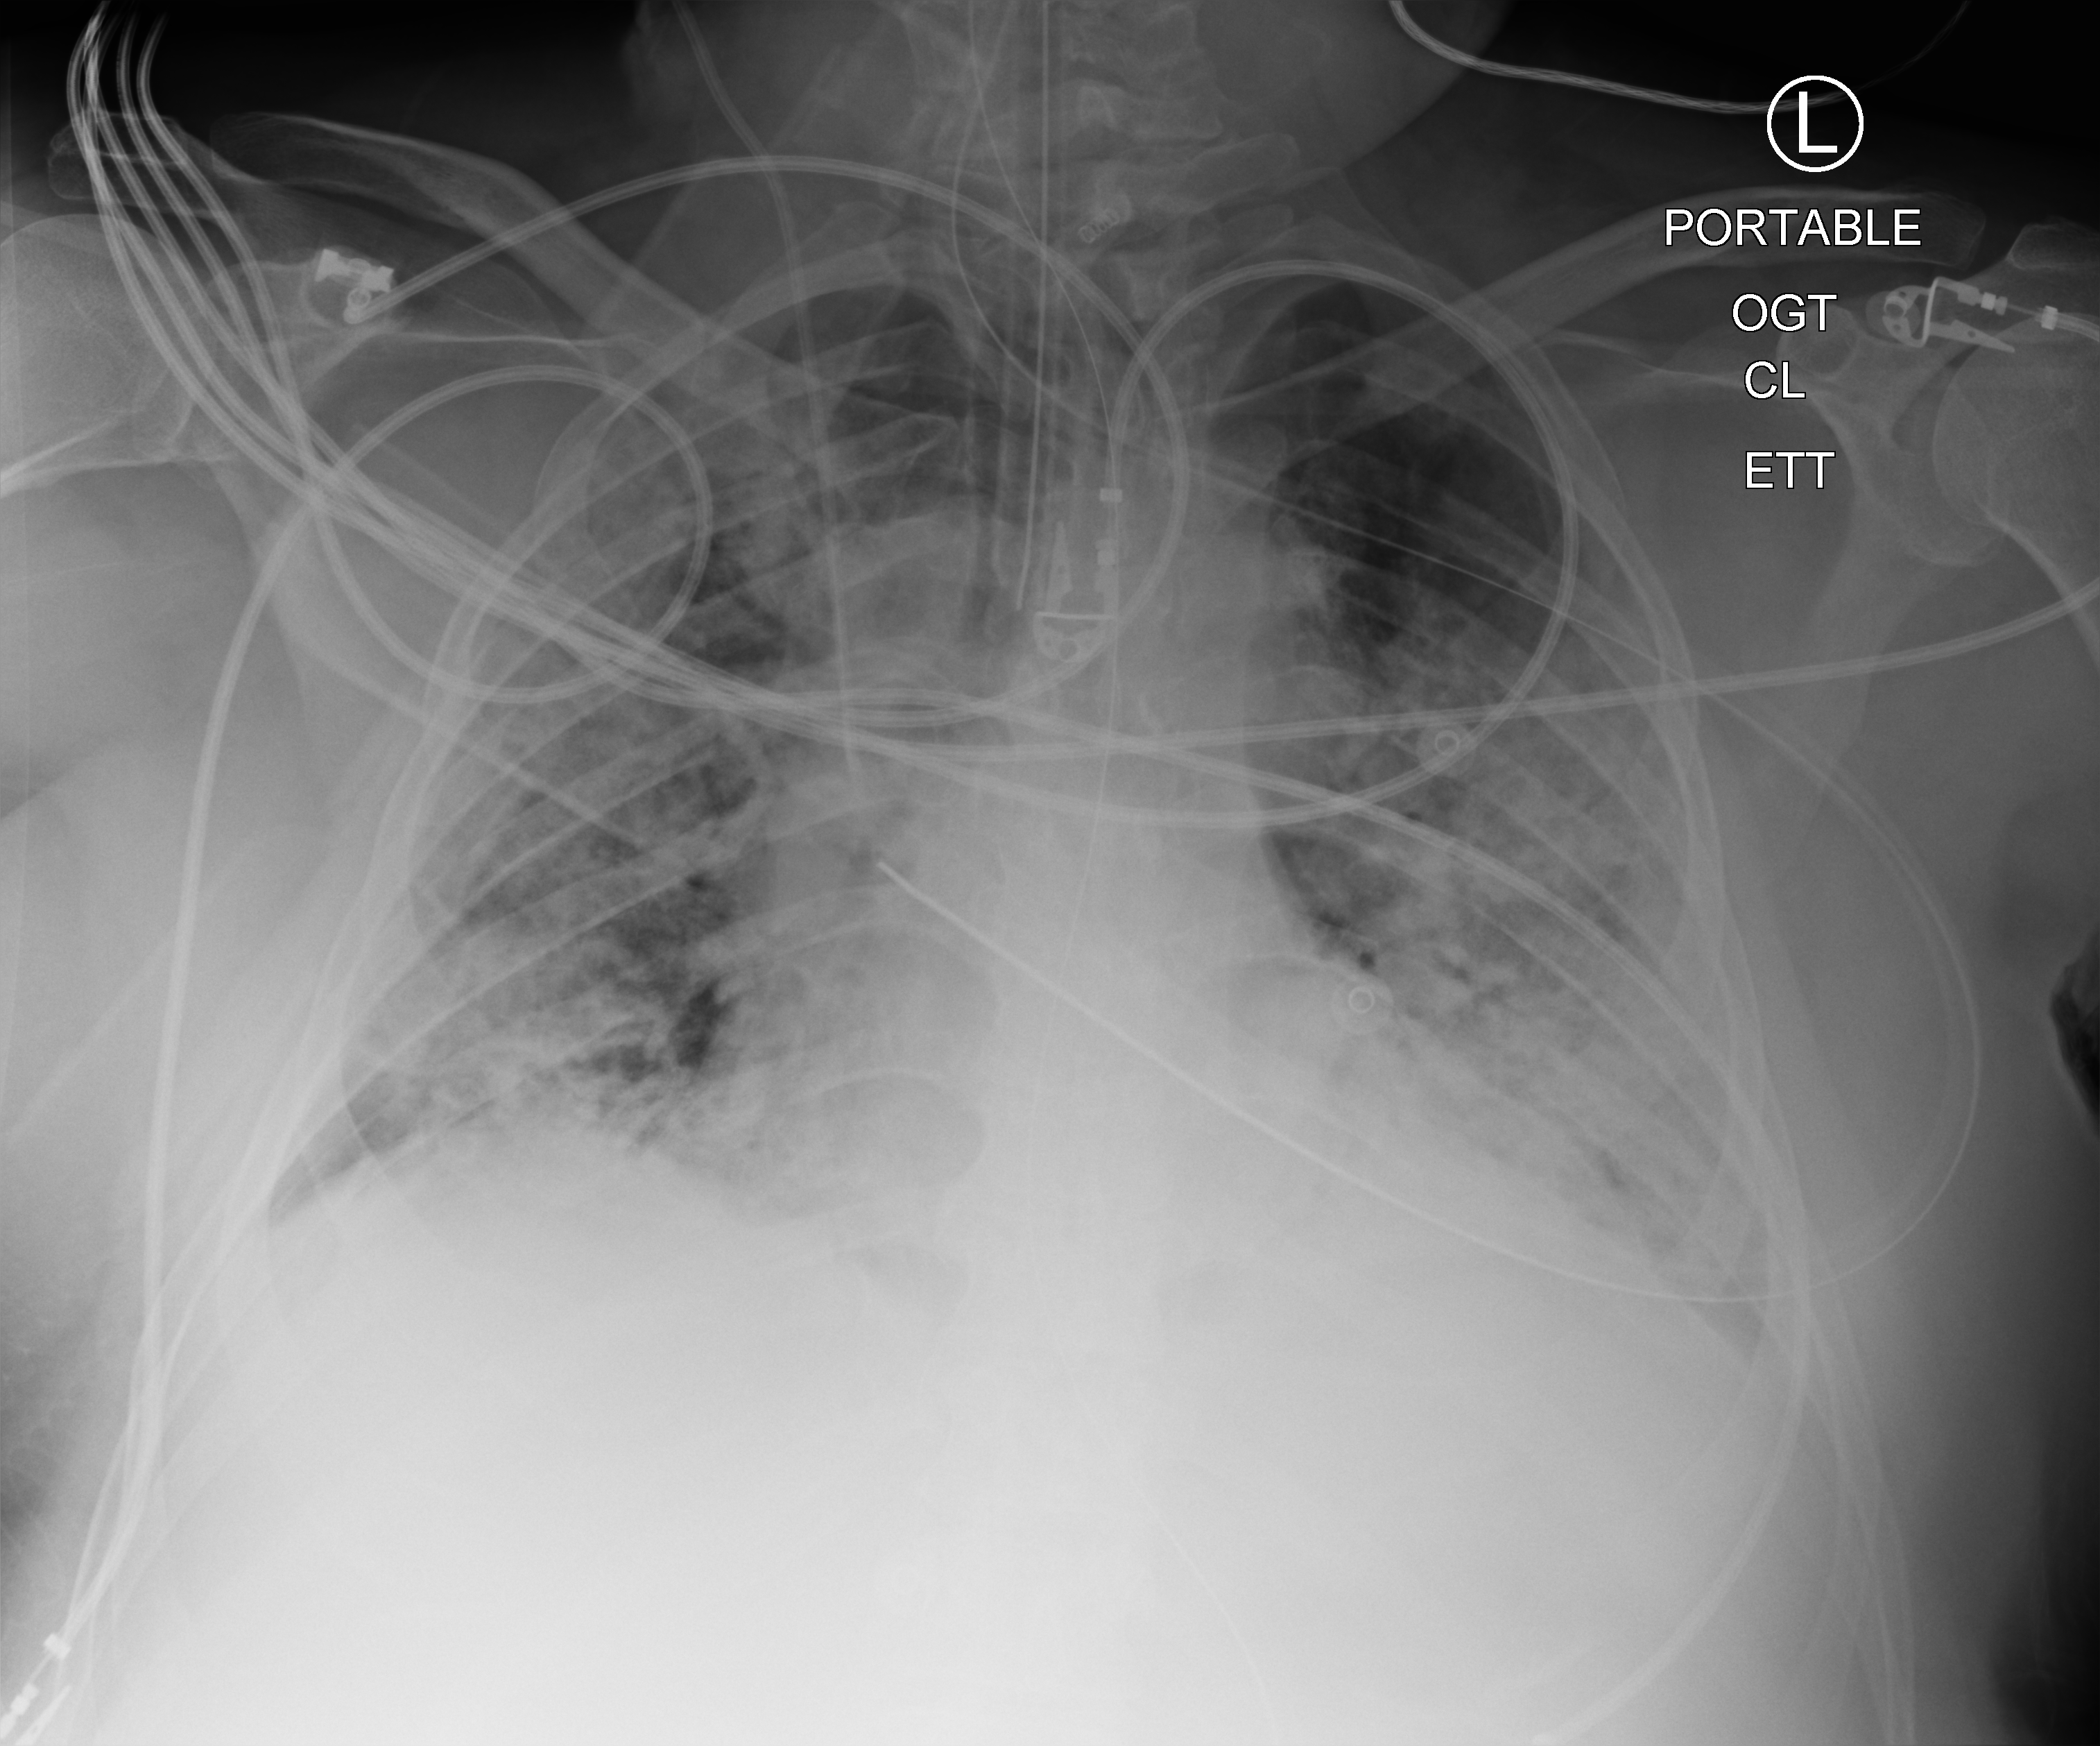
Portable chest radiograph; anteroposterior (AP) projection. Male patient hospitalised with COVID-19, age 18–59 years.
From the hospital-stay record, not from the radiograph (when in the stay this image was taken is not recorded): admitted to intensive care during this hospital stay: yes.